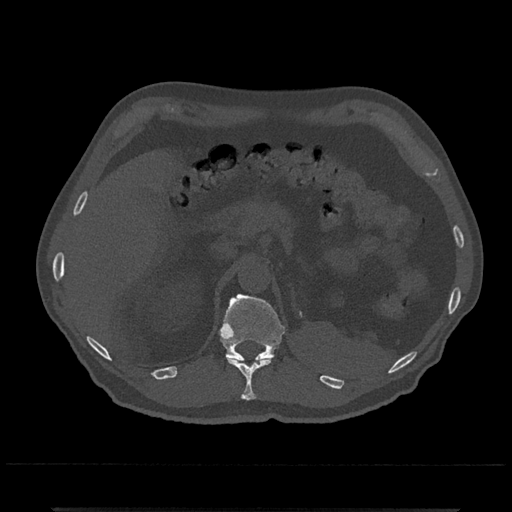
CT including the spine, one axial slice; position 455 of 797 along the scan axis; 120 kVp; bone window (W 1800 / L 400 HU); 0.5 mm slice thickness; 512 × 512 image matrix. Male patient, age 67 years. From the clinical record (not read from this slice): primary cancer: prostate.
Annotated regions visible in this slice (semi-automatically segmented with operator editing):
- T11 vertebra: box from (x=227, y=356) to (x=274, y=400) px
- T12 vertebra: (x=218, y=294)–(x=285, y=362)